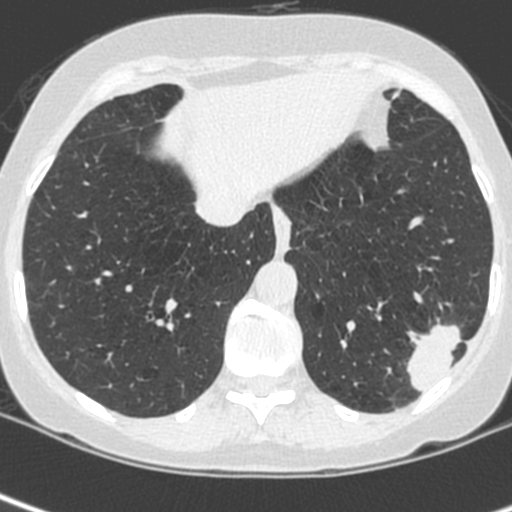
Low-dose screening chest CT, axial slice; baseline screening round; lung window (W 1500 / L -600 HU); 1.3 mm slice thickness; standard (soft-tissue) reconstruction kernel (C); 512 × 512 image matrix, field of view 271 × 271 mm. Female, age 56 years at enrolment.
• Expert reader's lesion annotation, bounding box (x1, y1, x2, y2) in pixels: (402, 310, 478, 387).
• Screening reader's record for this exam (one nodule recorded; not confirmed to be the boxed lesion): non-calcified nodule or mass ≥4 mm, left lower lobe, 37 × 29 mm, spiculated (stellate) margins, ground glass attenuation.
• Later outcome: lung cancer diagnosed 91 days after this screen — squamous cell carcinoma, NOS, left lower lobe, poorly differentiated (G3), stage IIIA (AJCC 6th edition), 35 mm at pathology.